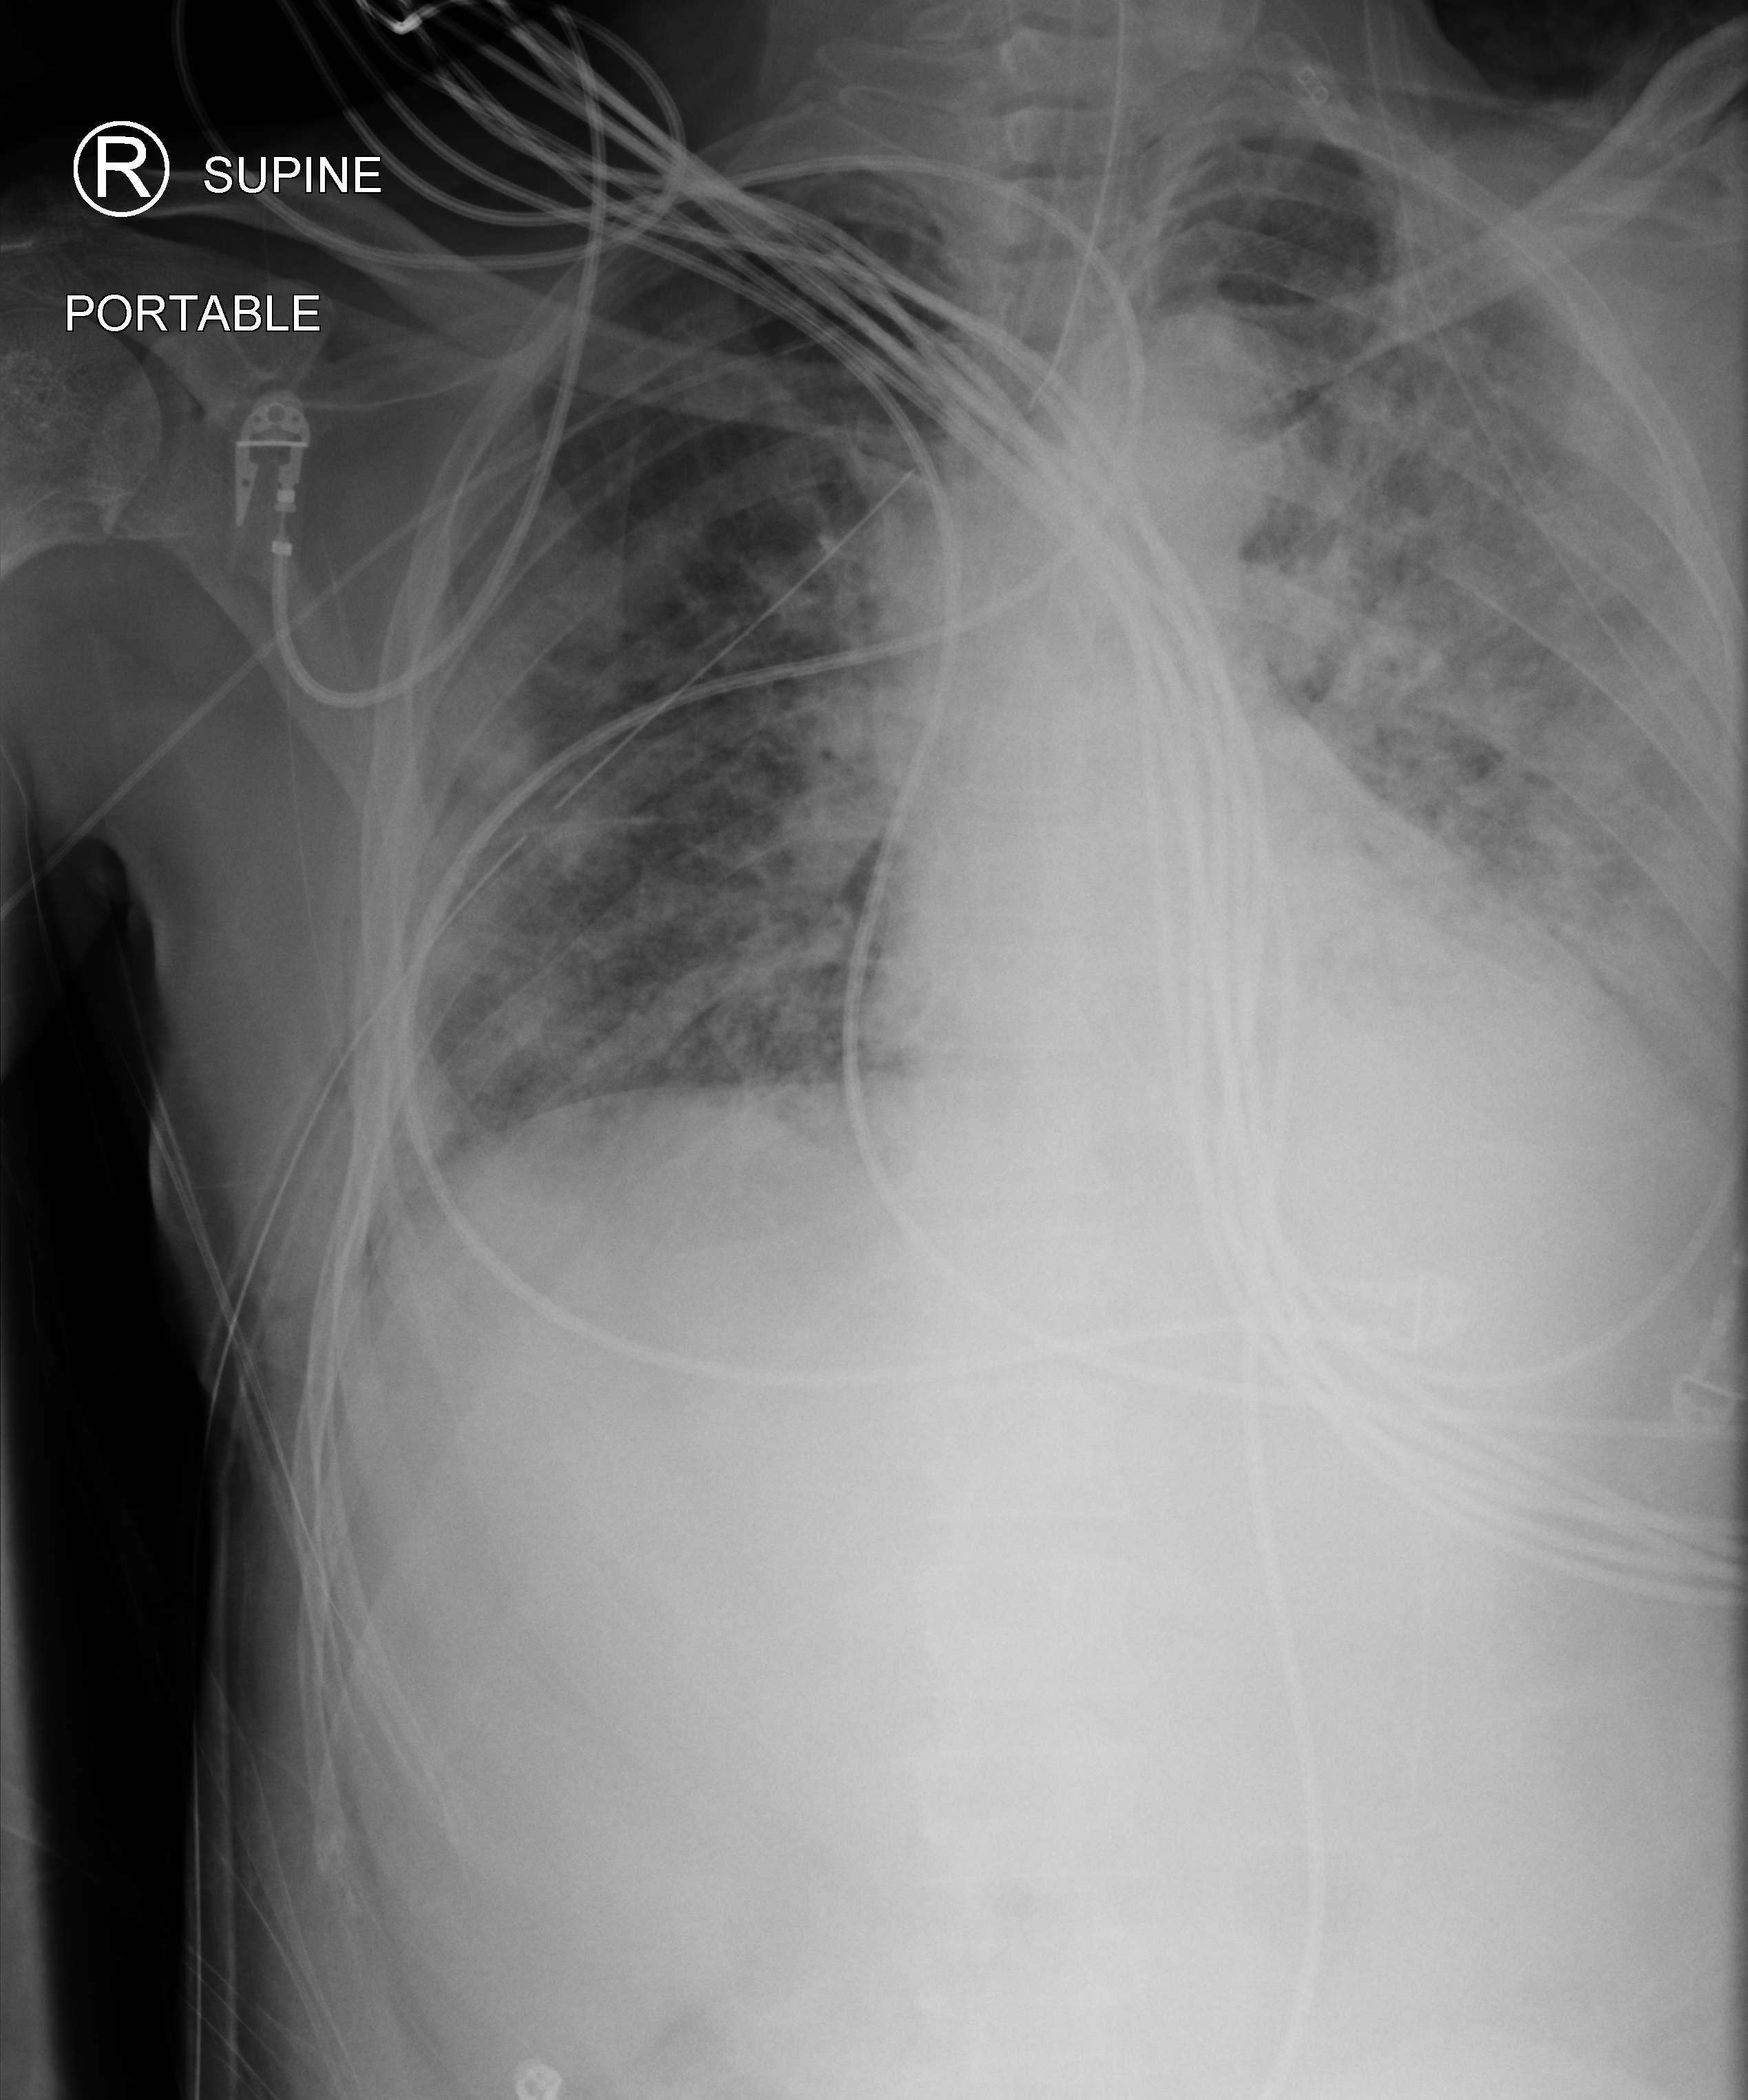
Bedside chest radiograph (computed radiography), anteroposterior (AP) projection. Patient hospitalised with COVID-19; male, aged 18–59 years.
Hospital-stay facts (about this admission, not read from this image; timing relative to this image not recorded):
- admitted to intensive care during this hospital stay: yes
- length of hospital stay: 41 days